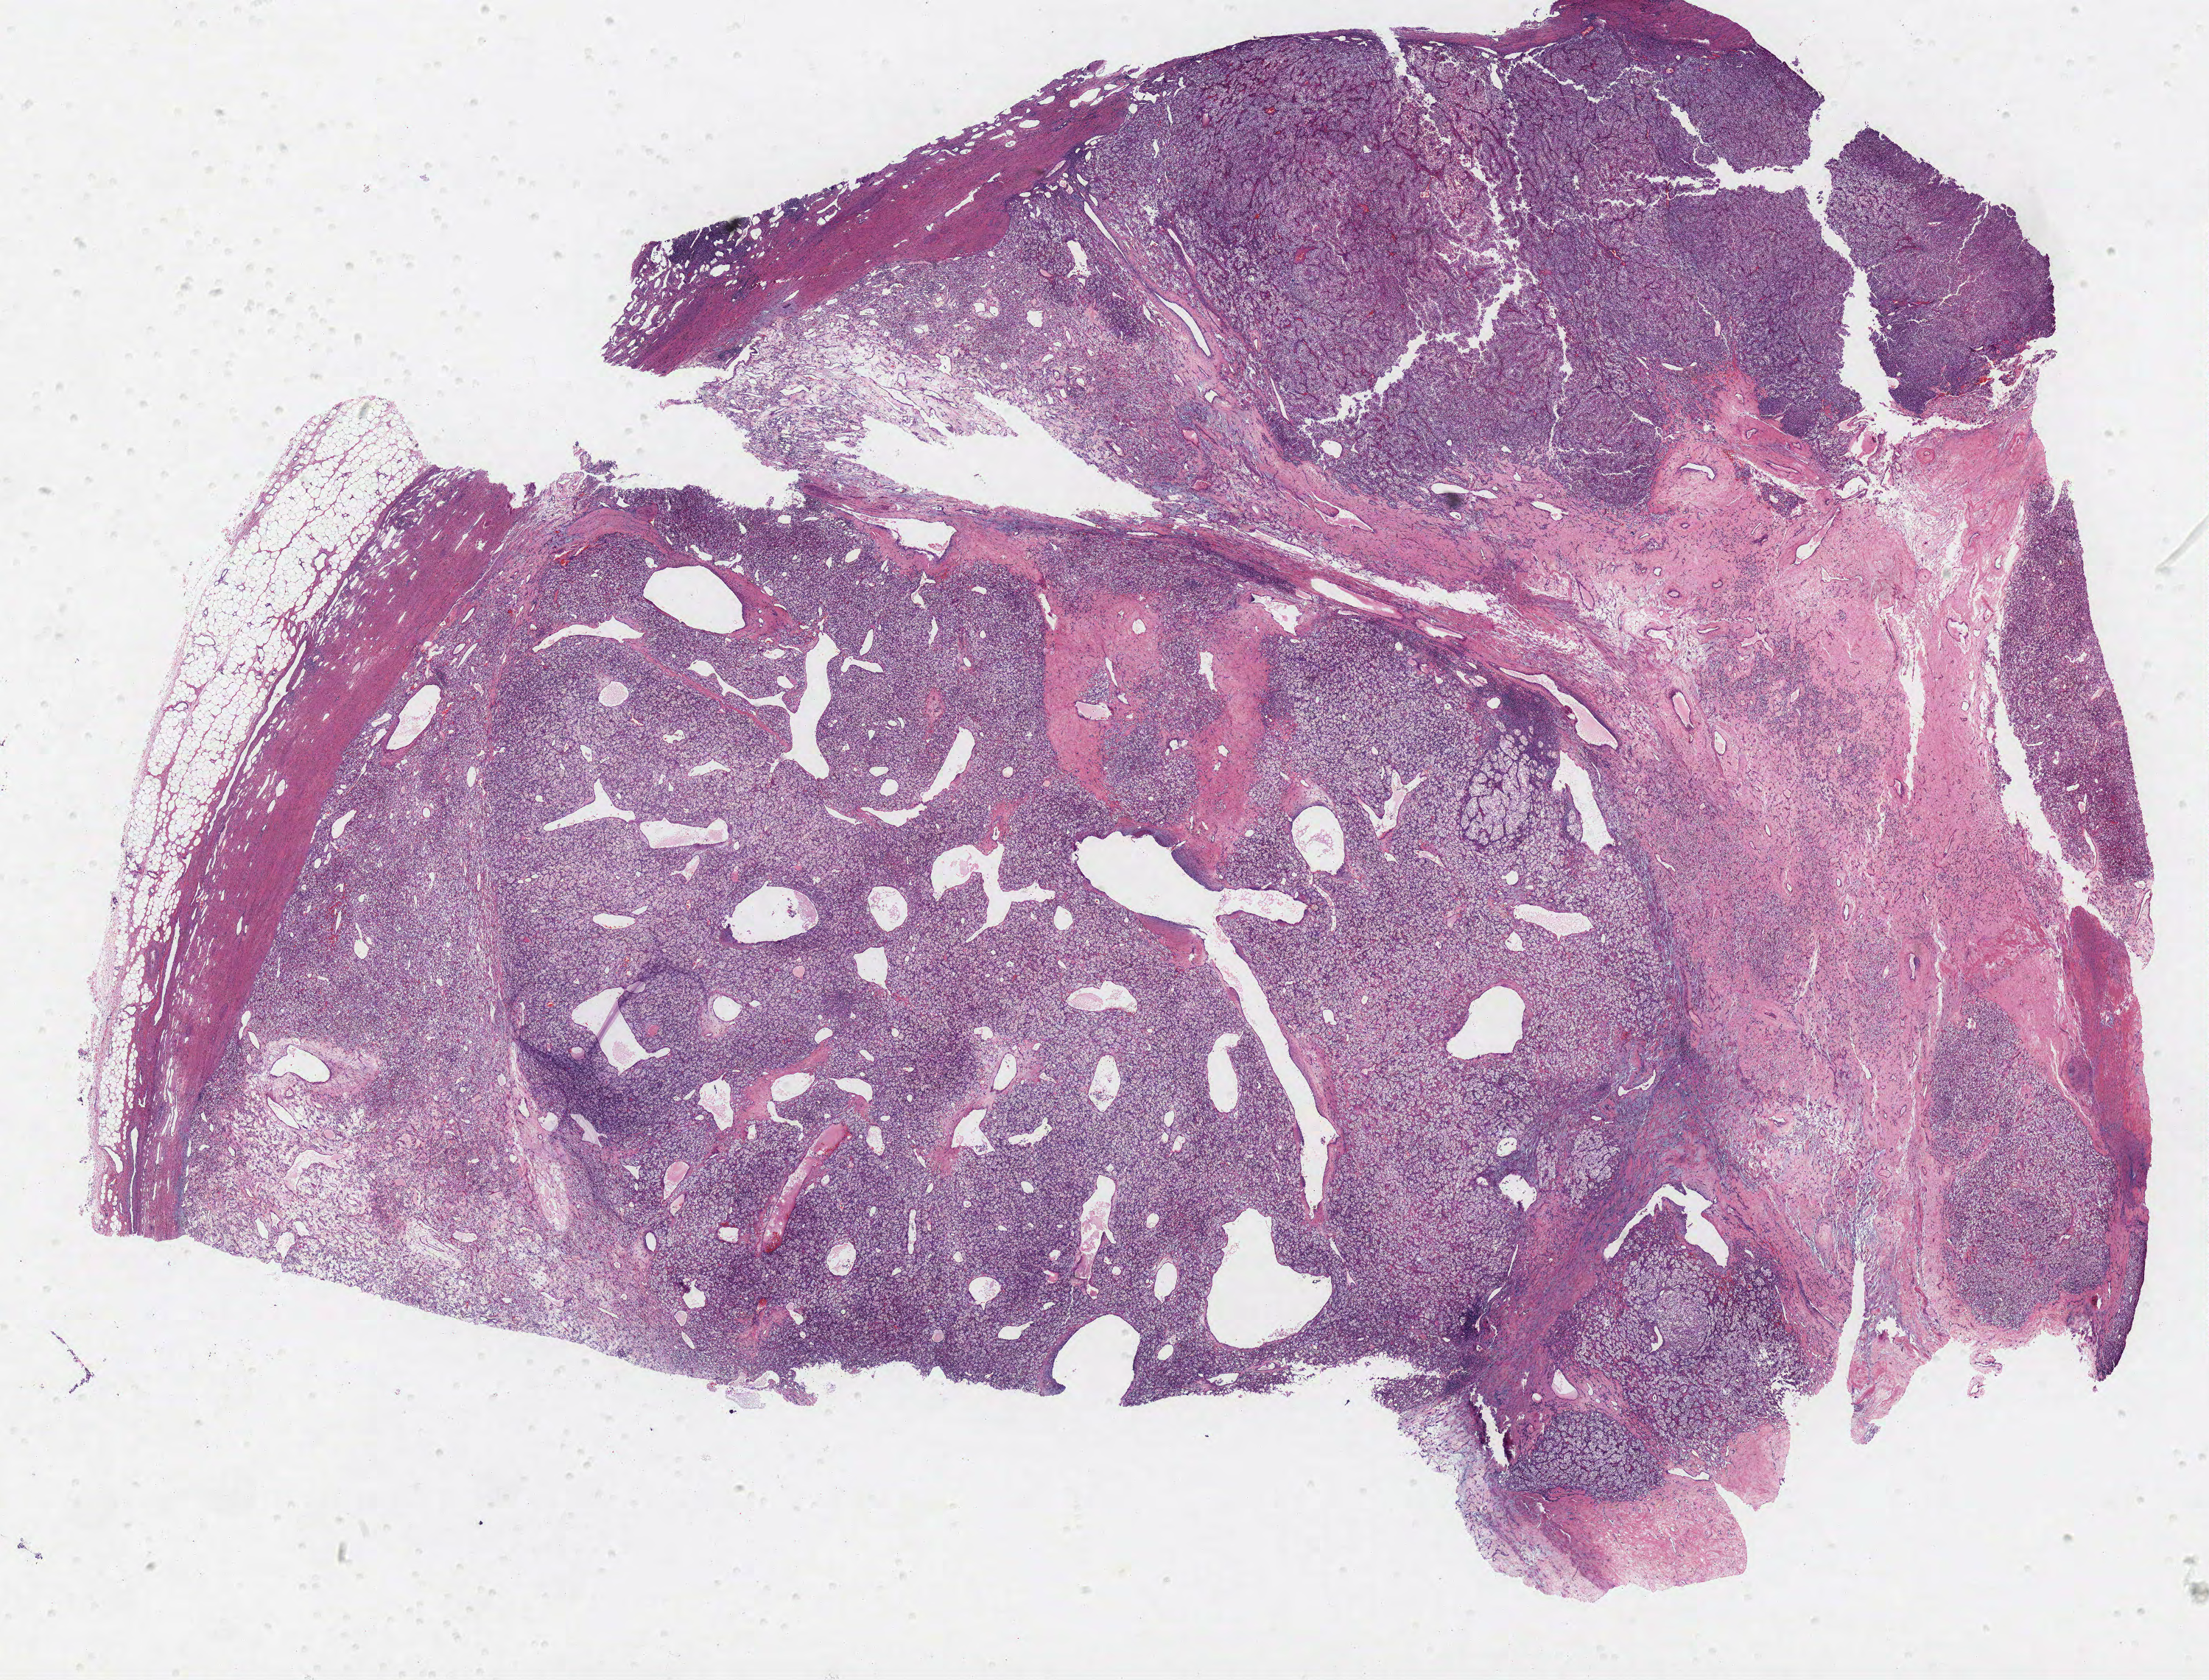
H&E-stained whole-slide image — low-resolution overview of the scanned area, about 24.0 x 18.2 mm; formalin-fixed paraffin-embedded (FFPE) diagnostic section; primary tumour sample from the kidney. Patient: male, age at initial diagnosis 57 years. Histologic grade: G3 (poorly differentiated).
- pathologic diagnosis: Clear cell adenocarcinoma, NOS
- AJCC pathologic stage: III
- TNM: T3b N0 M0
- lymph nodes positive (case pathology): 0 of 21 examined